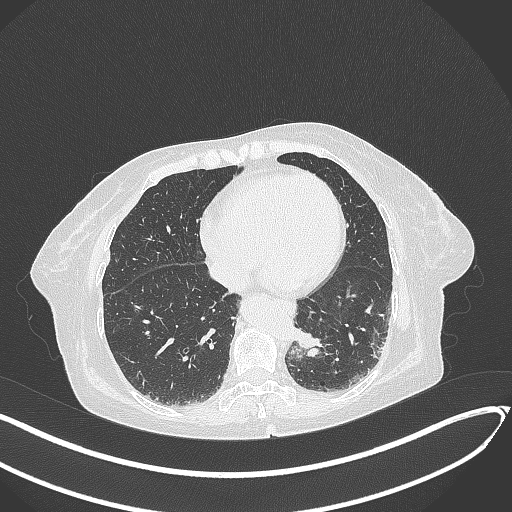
Chest CT, one axial slice; slice 67 of 324 in the series (ordered by position); reconstruction kernel B70f; 120 kVp; lung window (W 1500 / L -600 HU); 512 × 512 image matrix, field of view 400 × 400 mm. Patient: female, 82 years. Case-level facts recorded for this patient, not image findings: clinical TNM (as recorded): T1b N0 M1.
Structures marked on this image (rectangle marked by the reading radiologist):
- lung tumour (recorded histology: adenocarcinoma): bounding box (x1, y1, x2, y2) in pixels: (293, 325, 323, 357)